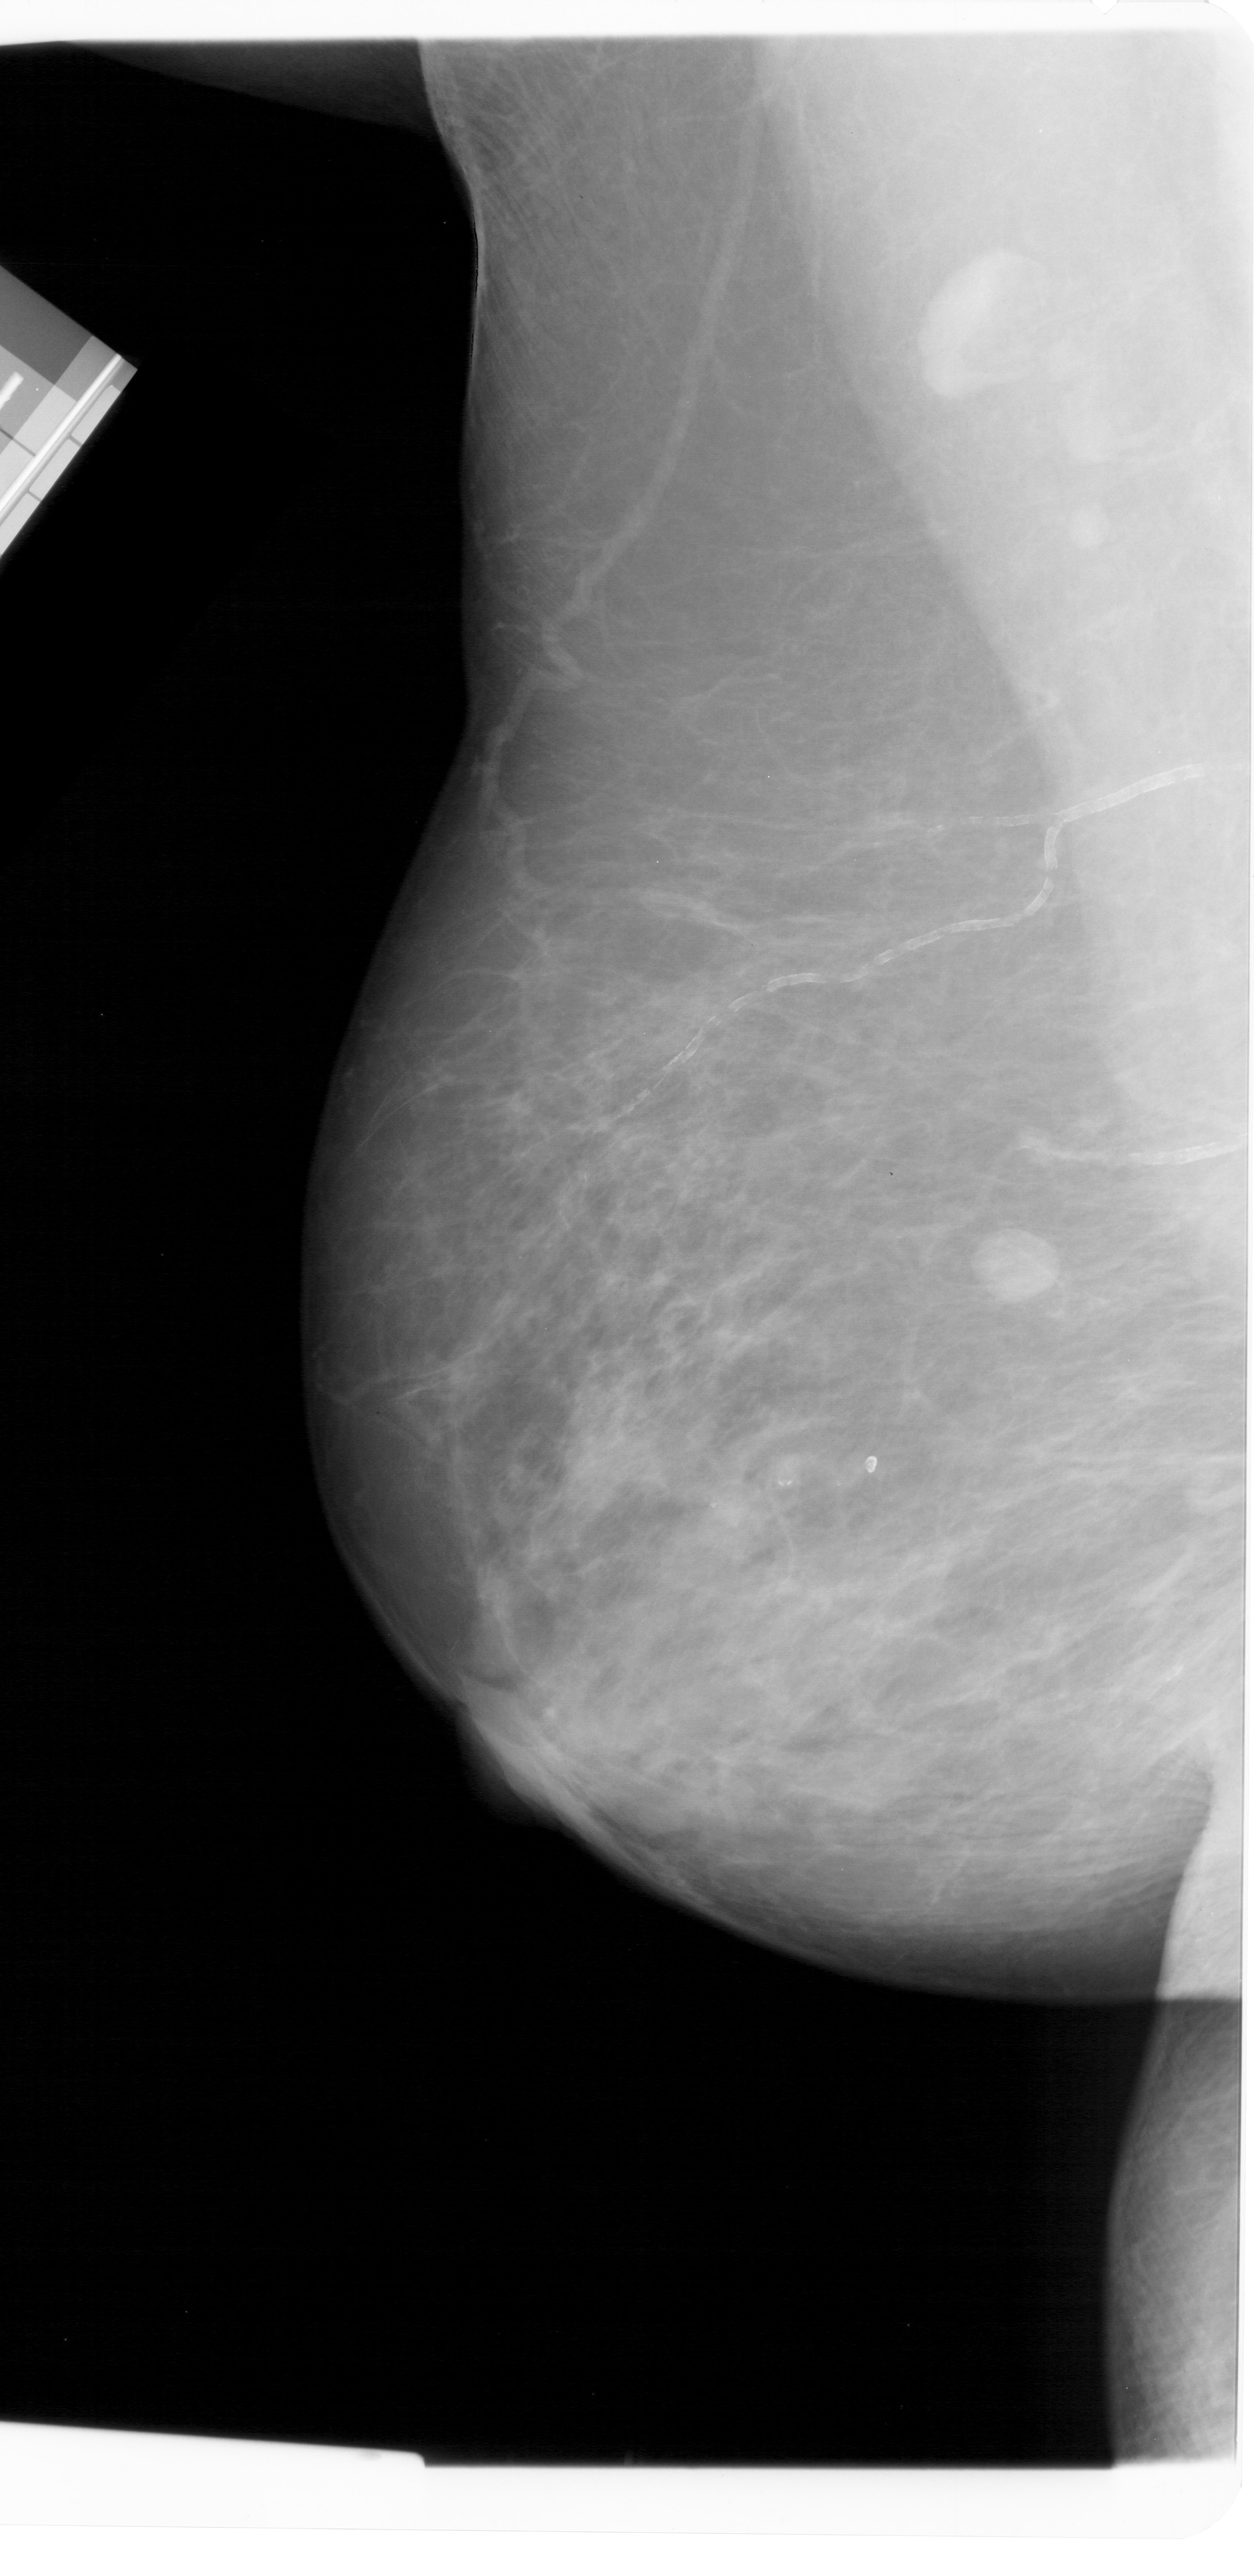
Scanned film-screen mammogram; left breast; MLO view; BI-RADS breast density category 2 (scale 1–4).
- Abnormality record for this image: mass, shape round, margins circumscribed; BI-RADS assessment category 3; pathology (as recorded): benign.